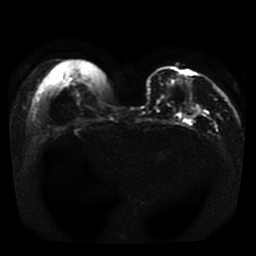
Breast MRI, one axial slice; position 9 of 41 along the scan axis; diffusion-weighted series; image 2 of 4 stored at this slice position (different b-values; order by instance number); 1.5 T; 256 × 256 image matrix. Female patient.
Structures marked on this image (outlined manually by an expert reader):
- tumour on diffusion-weighted imaging: bounding box [x1, y1, x2, y2] px = [185, 103, 200, 118]